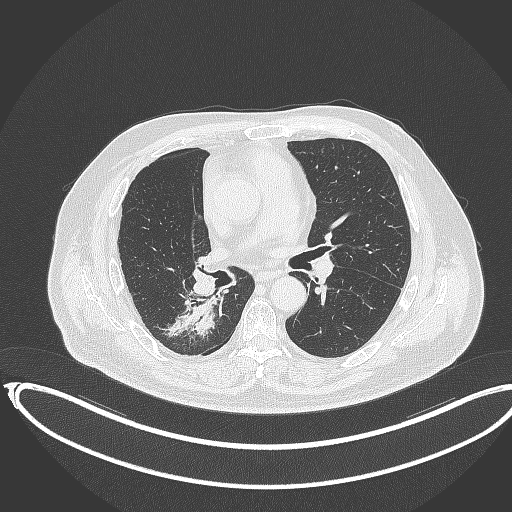
Chest CT, one axial slice. Position 188 of 403 along the scan axis. Lung window (W 1500 / L -600 HU). 1 mm slice thickness. 512 × 512 image matrix. Male patient, age 68 years. Case-level facts recorded for this patient, not image findings: clinical TNM (as recorded): T2a N0 M0.
Outlined on this slice (rectangle marked by the reading radiologist):
- lung tumour (recorded histology: adenocarcinoma): bounding box (x1, y1, x2, y2) in pixels: (161, 289, 229, 342)